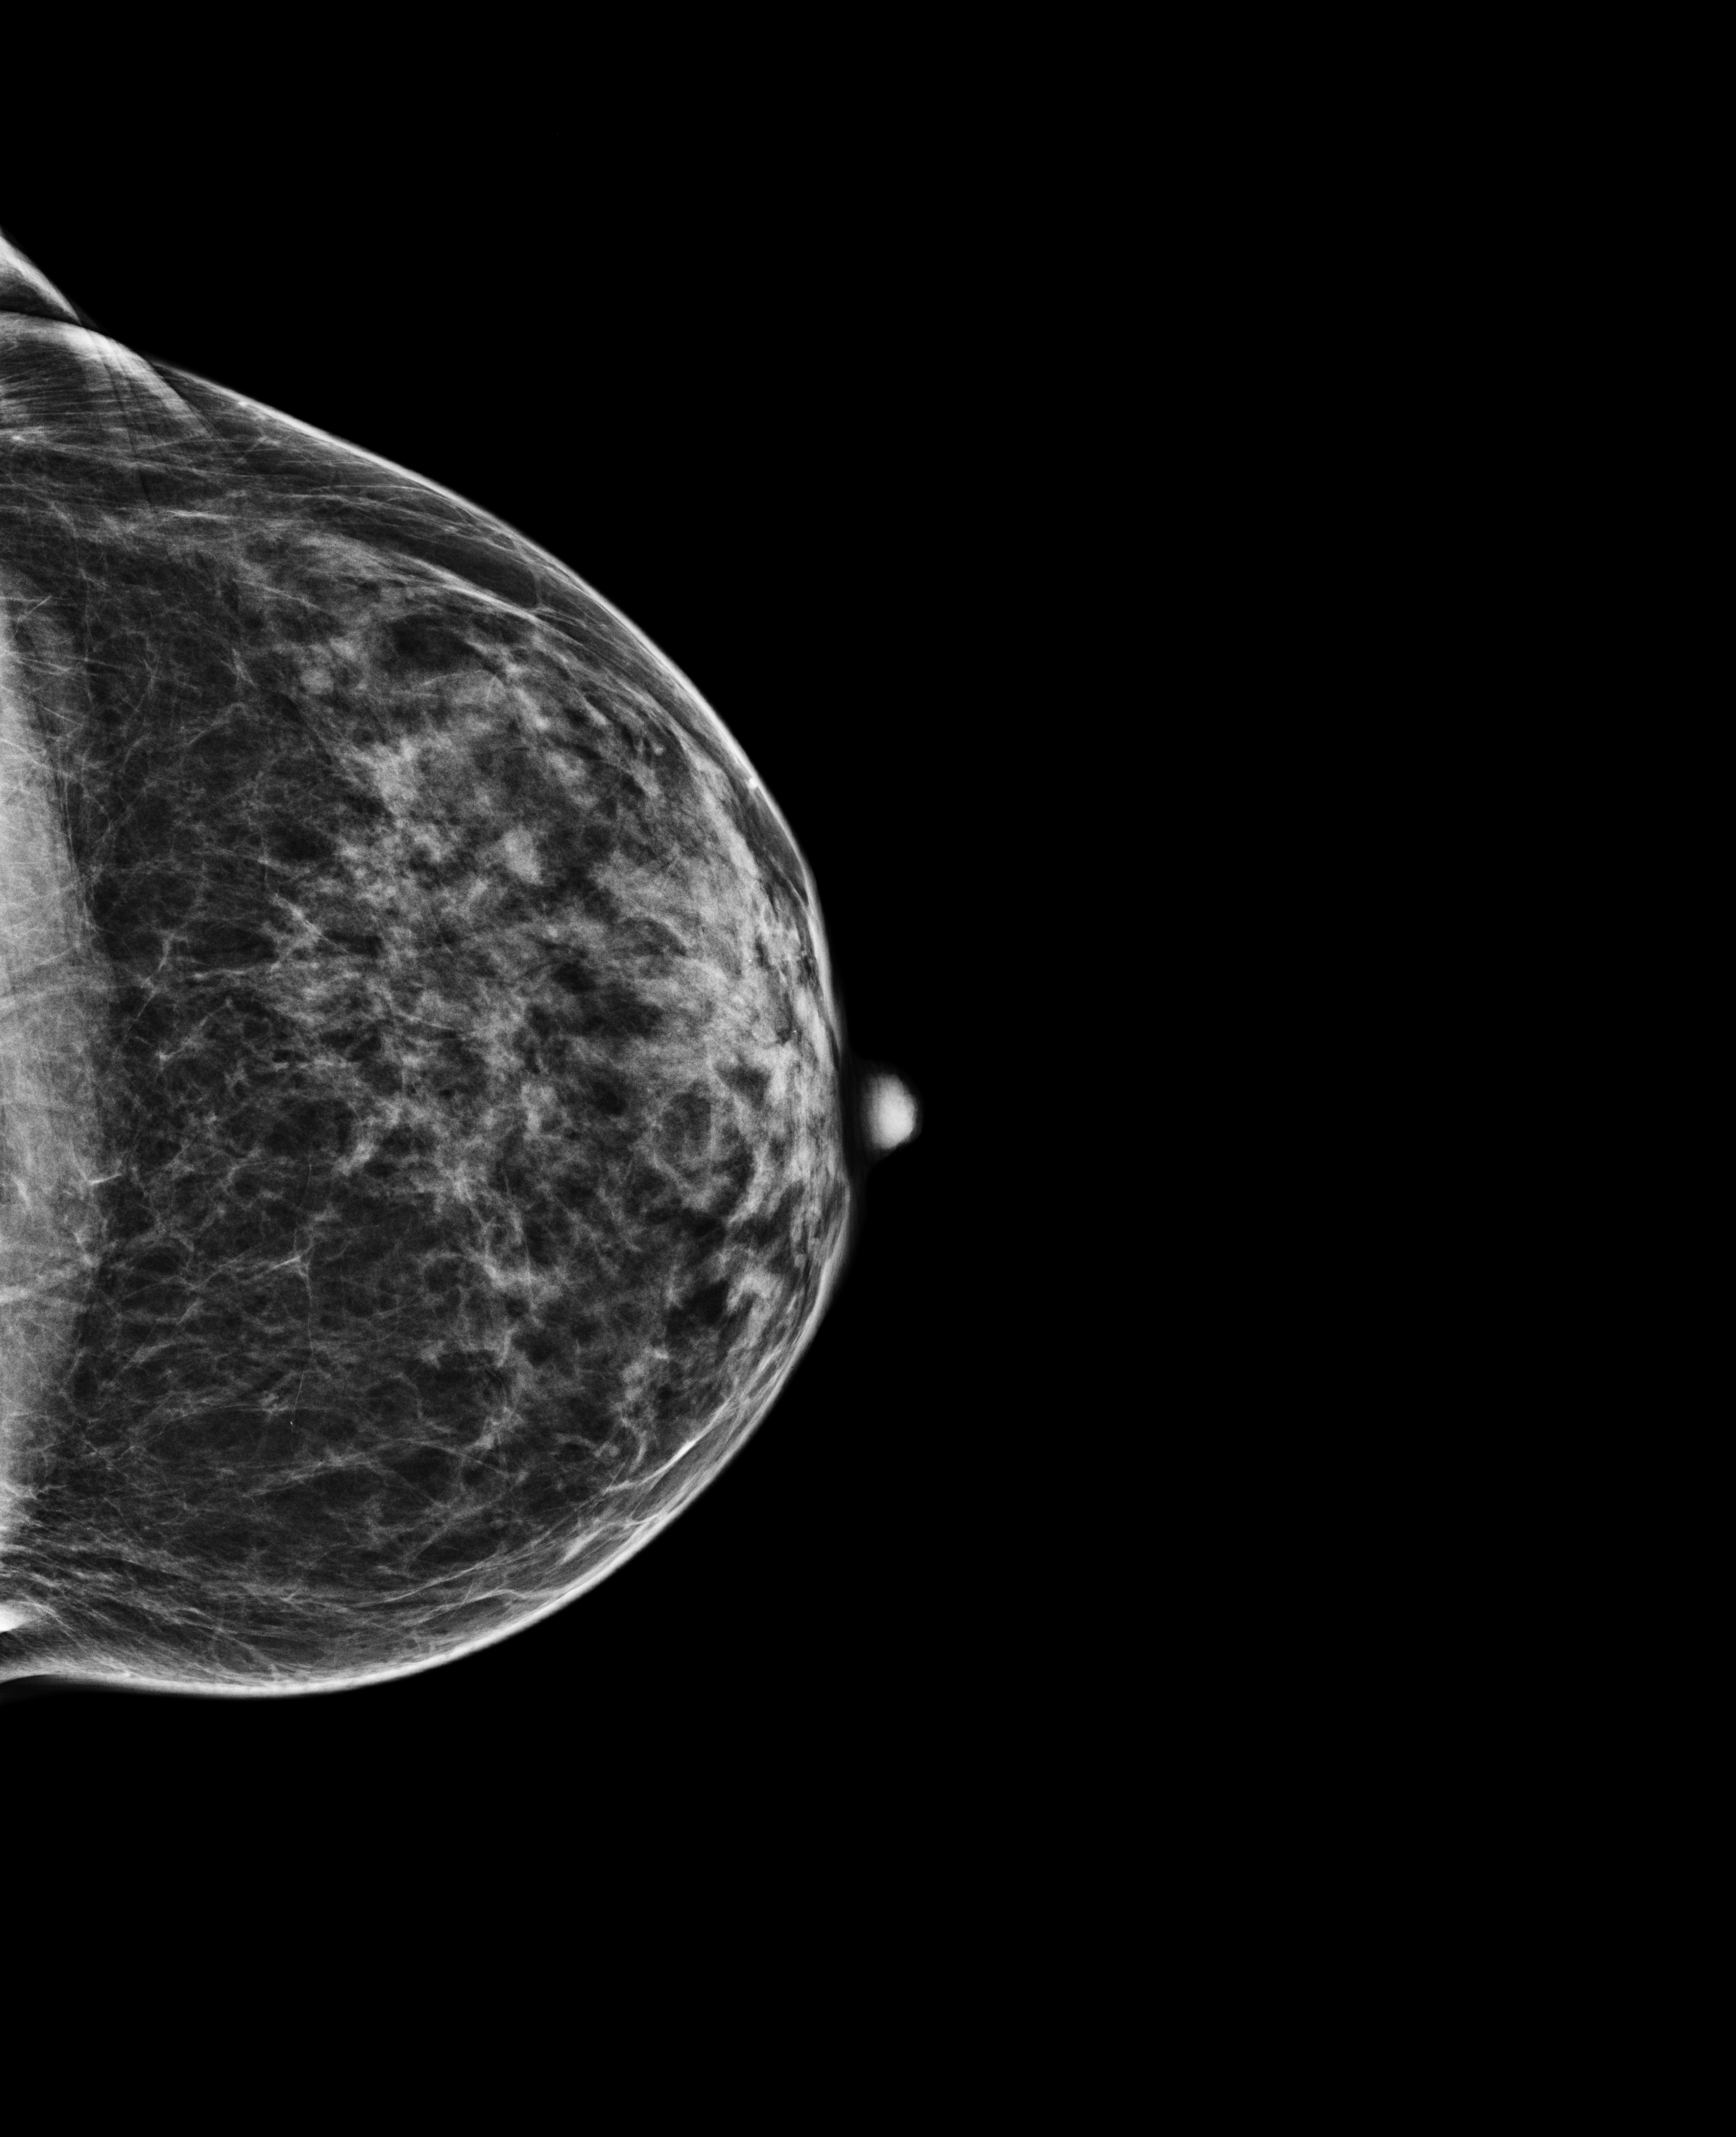
Annual screening mammography examination. Patient aged 51 years (female).
Image type: full-field digital mammogram. Breast: left. Projection: CC view.